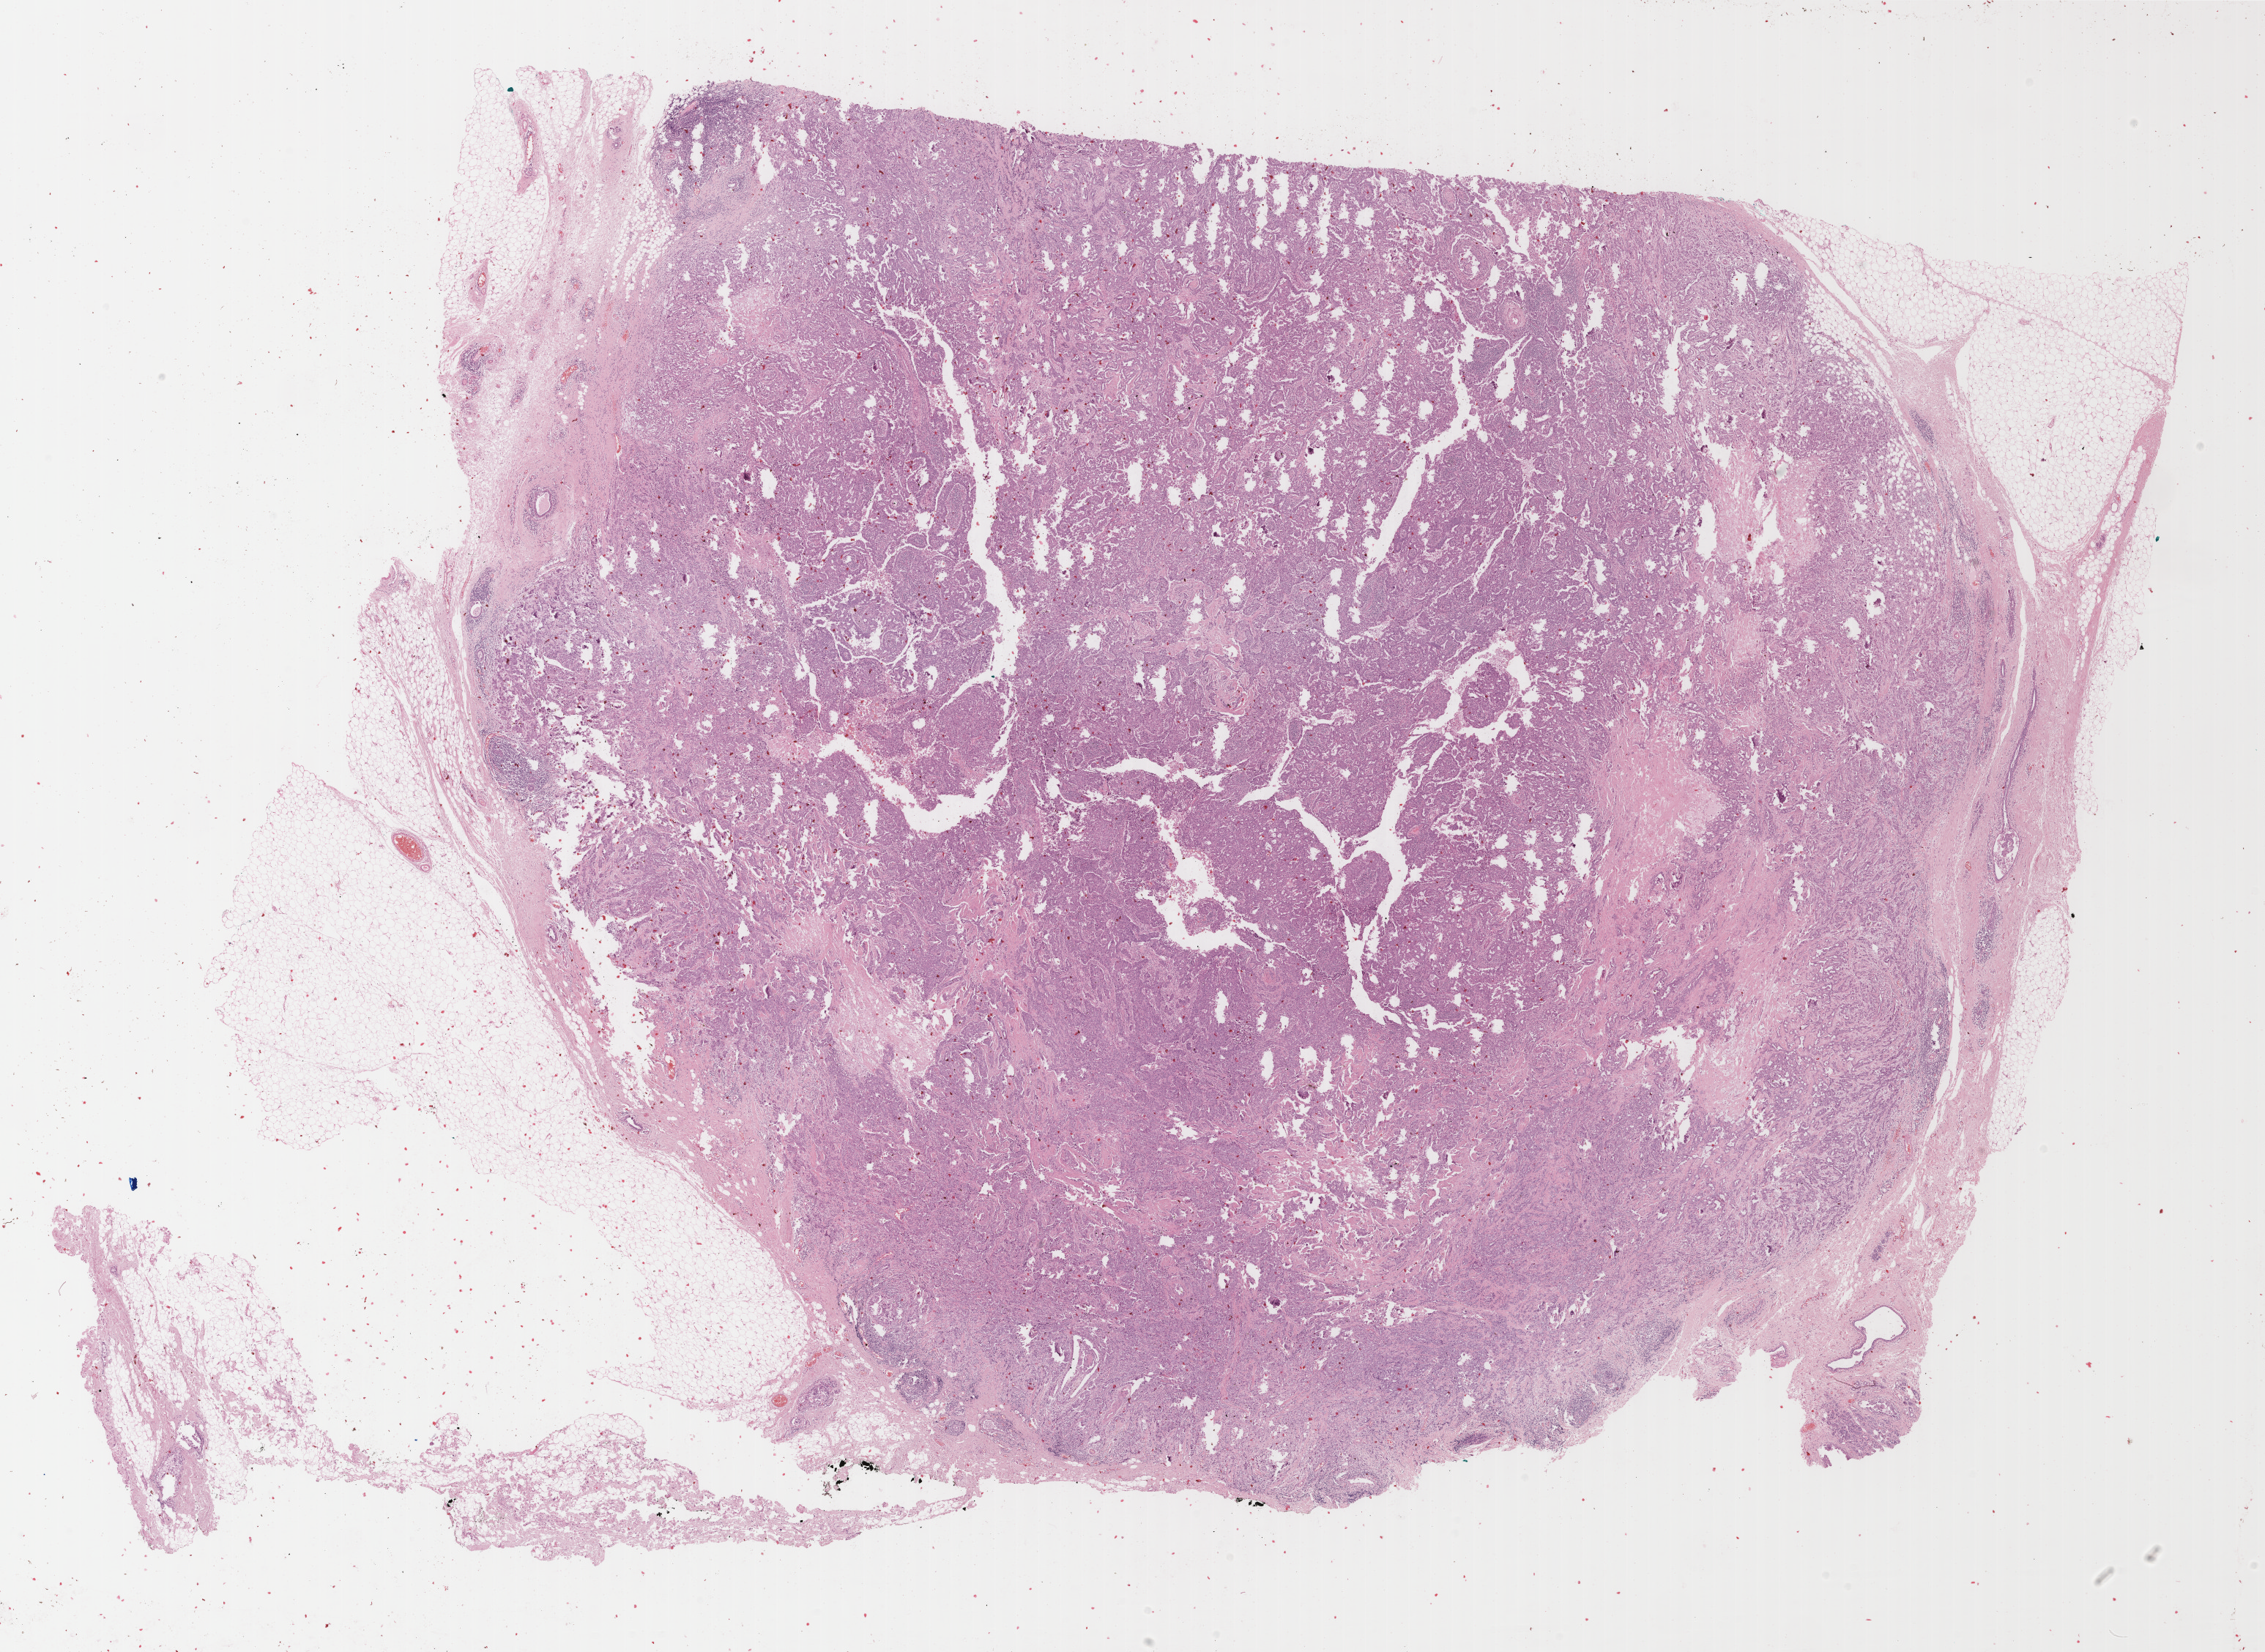
Whole-slide histology image, H&E-stained — whole scanned area (about 24.6 x 17.9 mm, acquisition: 40x scan) shown as a low-resolution overview. Formalin-fixed paraffin-embedded (FFPE) diagnostic section. Sample: primary tumour, breast. Female, age 45 years at initial diagnosis.
Lymph nodes positive (case pathology): 0 of 1 examined. Histologic diagnosis: Infiltrating duct carcinoma, NOS.